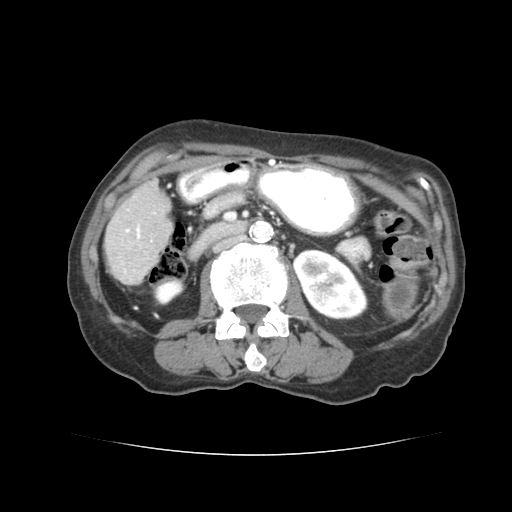
Contrast-enhanced abdominal CT (liver protocol), one axial slice. Position 16 of 77 along the scan axis. Reconstruction kernel STANDARD. 120 kVp. Soft-tissue window (W 400 / L 40 HU). 2.5 mm slice thickness. 512 × 512 image matrix, field of view 340 × 340 mm. Case-level facts recorded for this patient, not image findings: diagnosis: hepatocellular carcinoma (patient treated with transarterial chemoembolisation; whether this scan precedes or follows treatment is not stated here); TNM stage (as recorded): Stage-I; Child-Pugh class: A; tumour size: 7.6 cm.
Outlined on this slice (semi-automatic segmentation, software-assisted and operator-edited):
- liver parenchyma outside the tumour (the mass and vessels are separate outlines, so this box may not span the whole liver): bounding box <104,170,168,280> (left, top, right, bottom; pixels)
- liver vessels: <132,213,152,241>